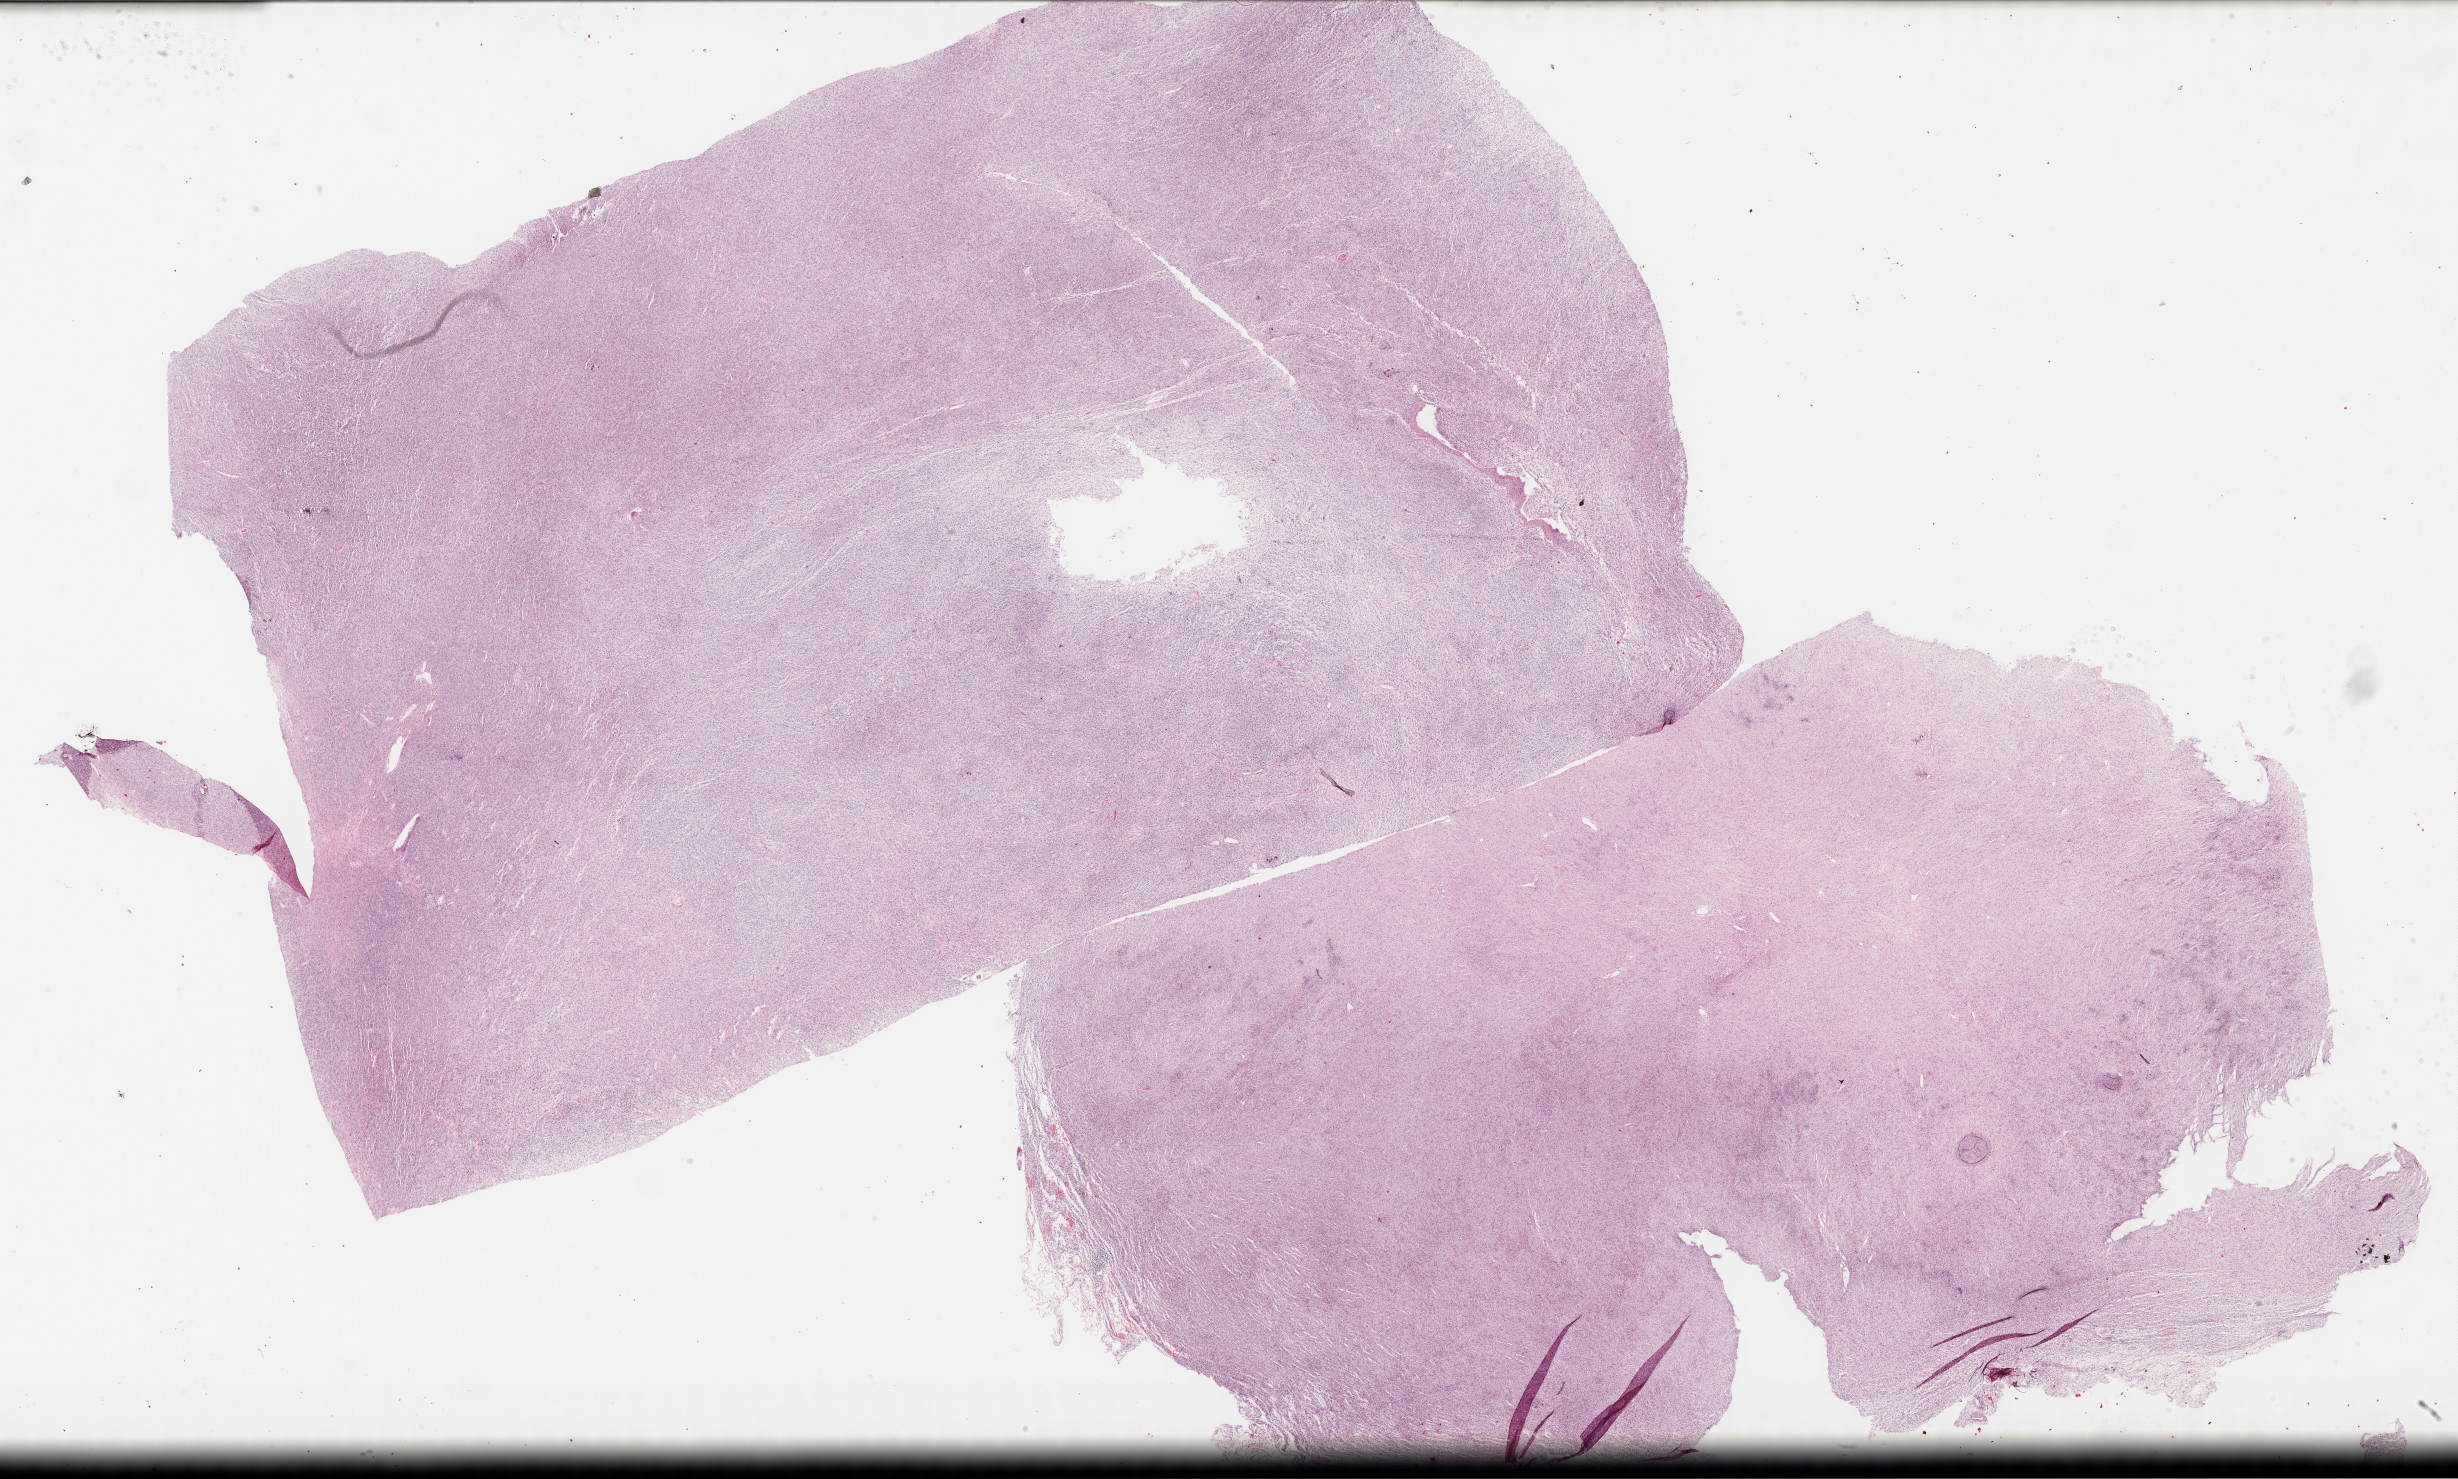
Whole-slide histology image, H&E-stained — low-resolution overview of the scanned area, about 39.8 x 23.9 mm. Formalin-fixed paraffin-embedded (FFPE) diagnostic section. Primary tumour sample from the retroperitoneum and peritoneum. Patient: male, age at initial diagnosis 66 years.
Diagnosis: Dedifferentiated liposarcoma (retroperitoneum).